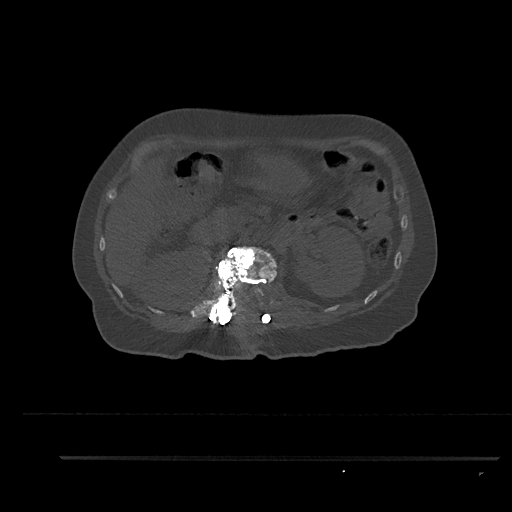
CT including the spine, one axial slice; 120 kVp; bone window (W 1800 / L 400 HU); 0.5 mm slice thickness; 512 × 512 image matrix, field of view 408 × 408 mm. Patient: female, 44 years. From the clinical record (not read from this slice): primary cancer: renal; vertebrae with lytic lesions (as recorded): L1.
Annotated regions visible in this slice (semi-automatic segmentation, software-assisted and operator-edited):
- L1 vertebra: box from (x=204, y=246) to (x=277, y=323) px